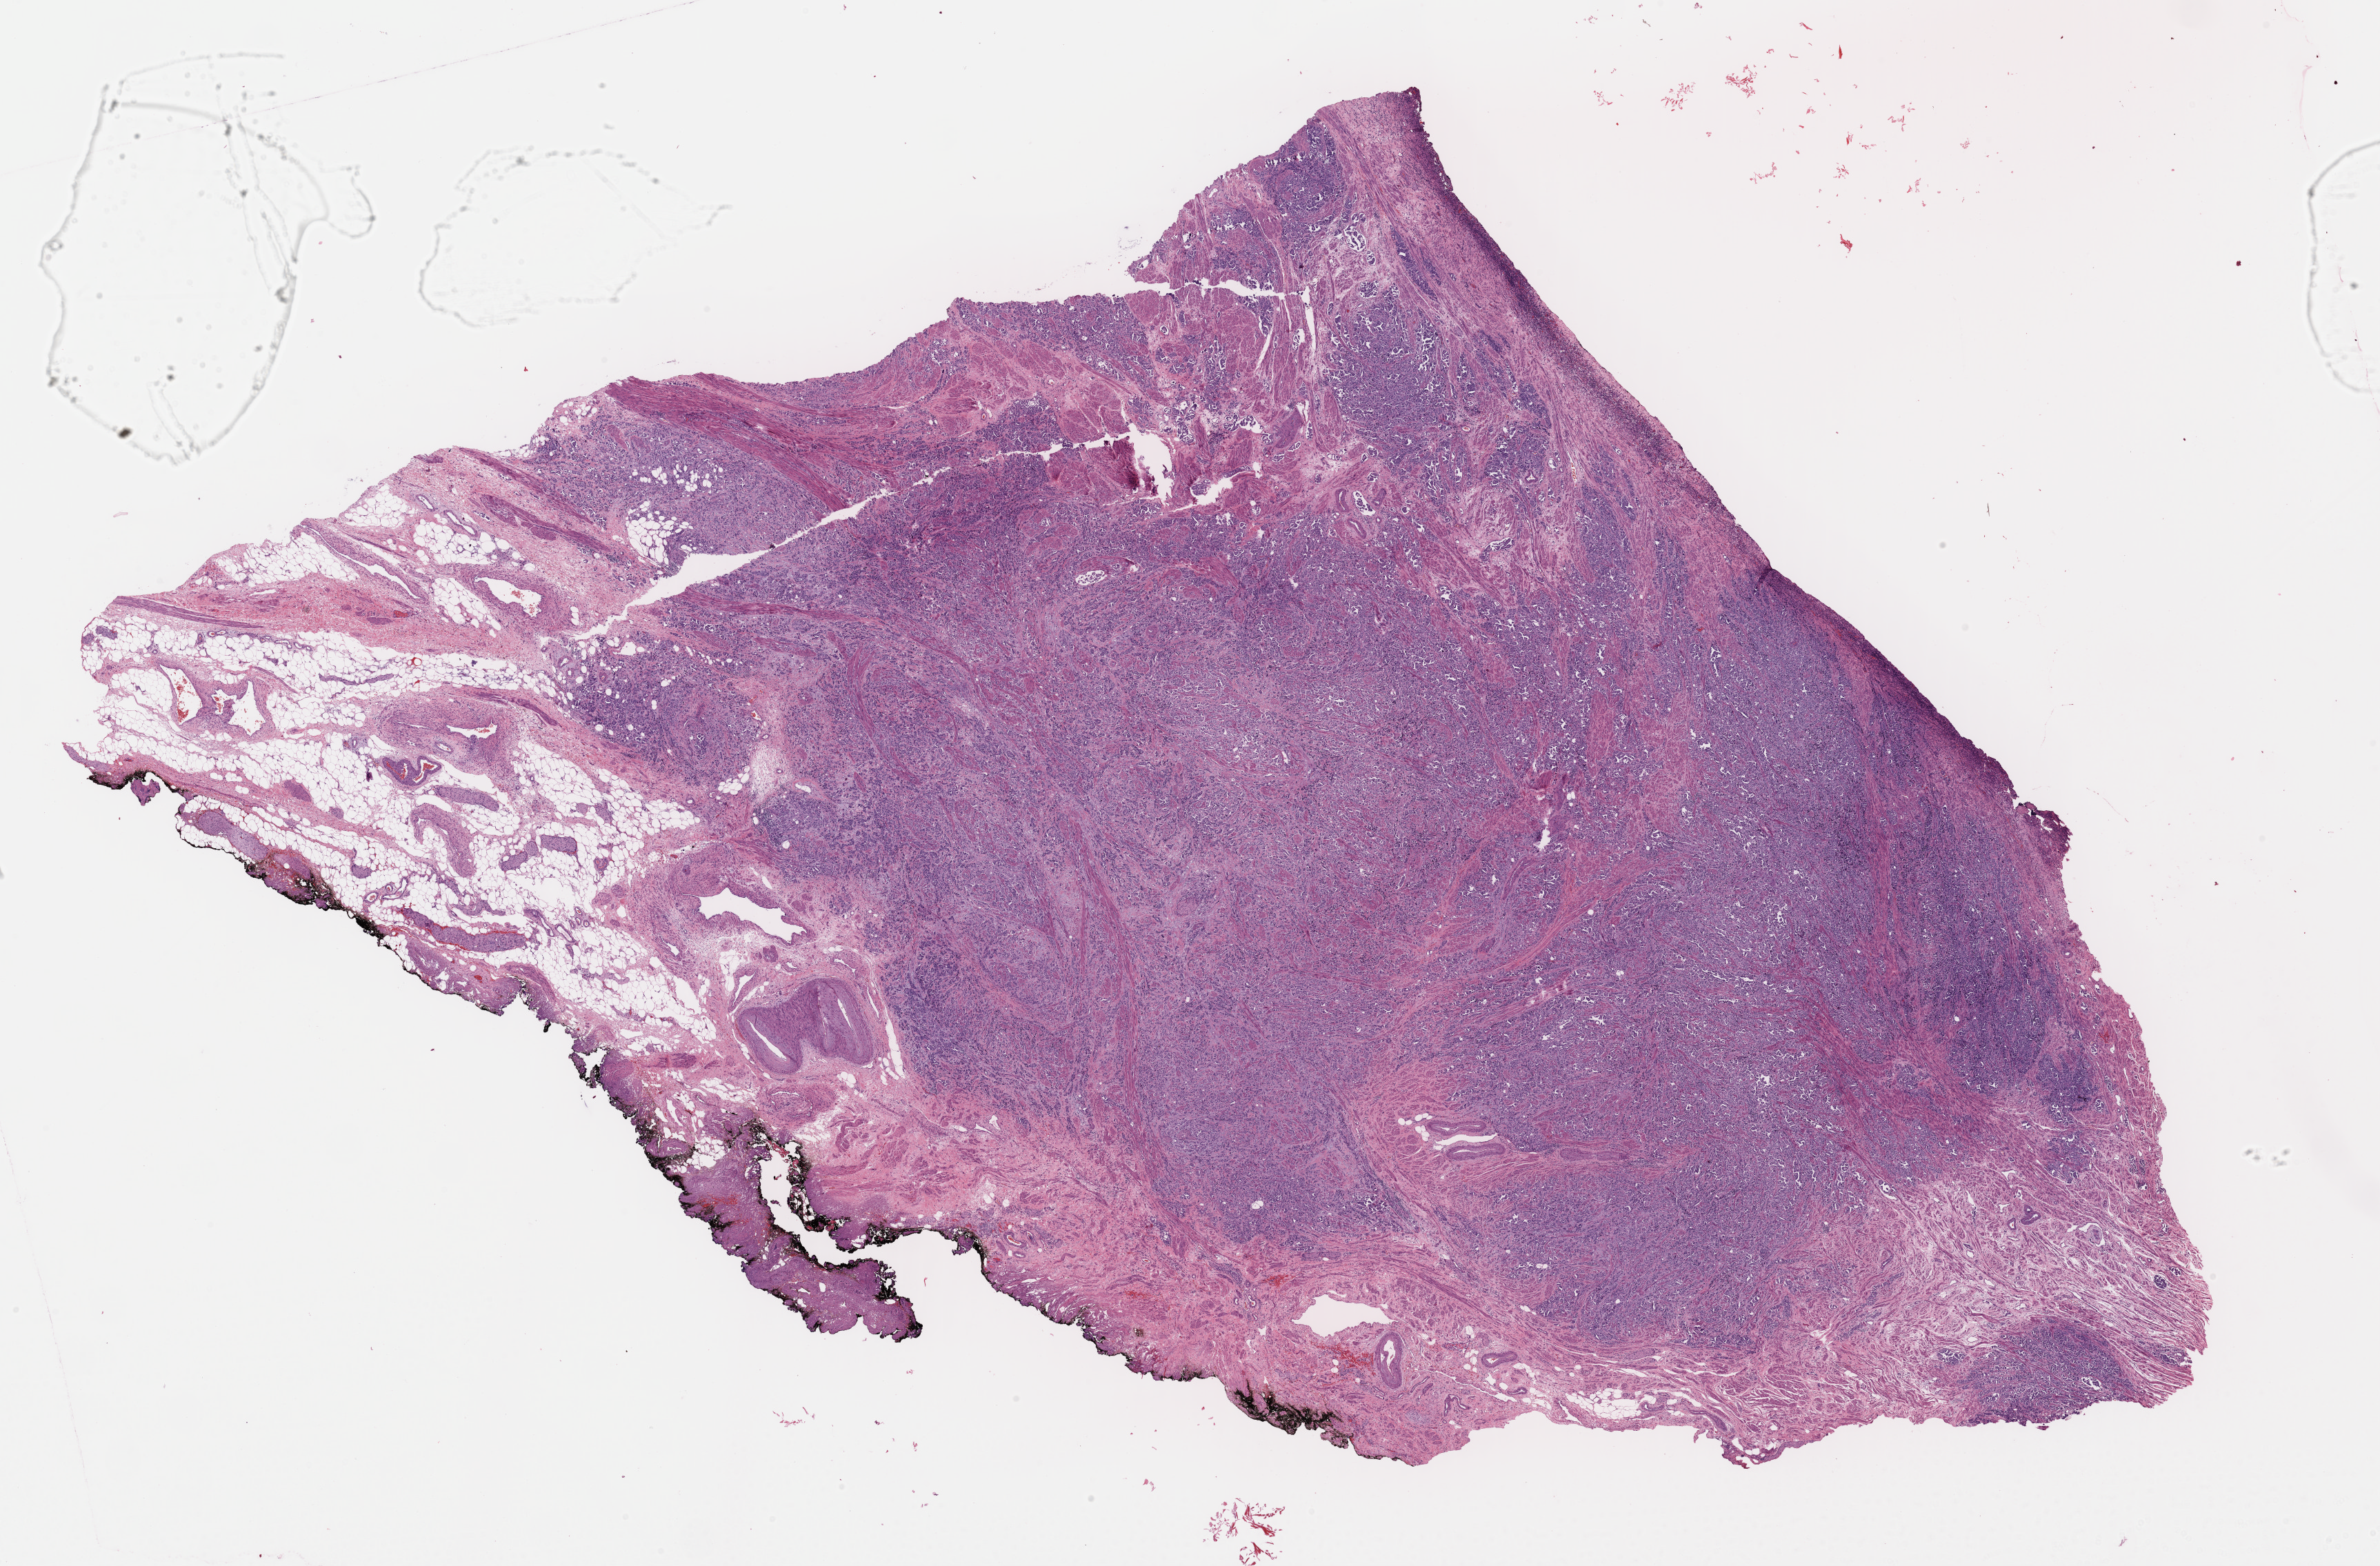
Whole-slide histology image, H&E, shown as a low-resolution overview of the whole scanned area (about 27.3 x 17.9 mm, slide scanned at 40x); formalin-fixed paraffin-embedded (FFPE) diagnostic section; sample: primary tumour, bladder. Patient: female, age at initial diagnosis 79 years. Histologic grade: high grade.
AJCC pathologic stage: IV. Diagnosis: Transitional cell carcinoma. TNM: T3b N1 M0.